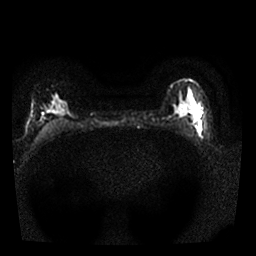
Breast MRI, one axial slice; slice 17 of 25 in the series (ordered by position); diffusion-weighted series; image 2 of 4 stored at this slice position (different b-values; order by instance number); 1.5 T; 4 mm slice thickness; 256 × 256 image matrix, field of view 300 × 300 mm. Female patient.
Outlined on this slice (expert manual segmentation):
- tumour on diffusion-weighted imaging: bounding box (x1, y1, x2, y2) in pixels: (194, 112, 202, 129)